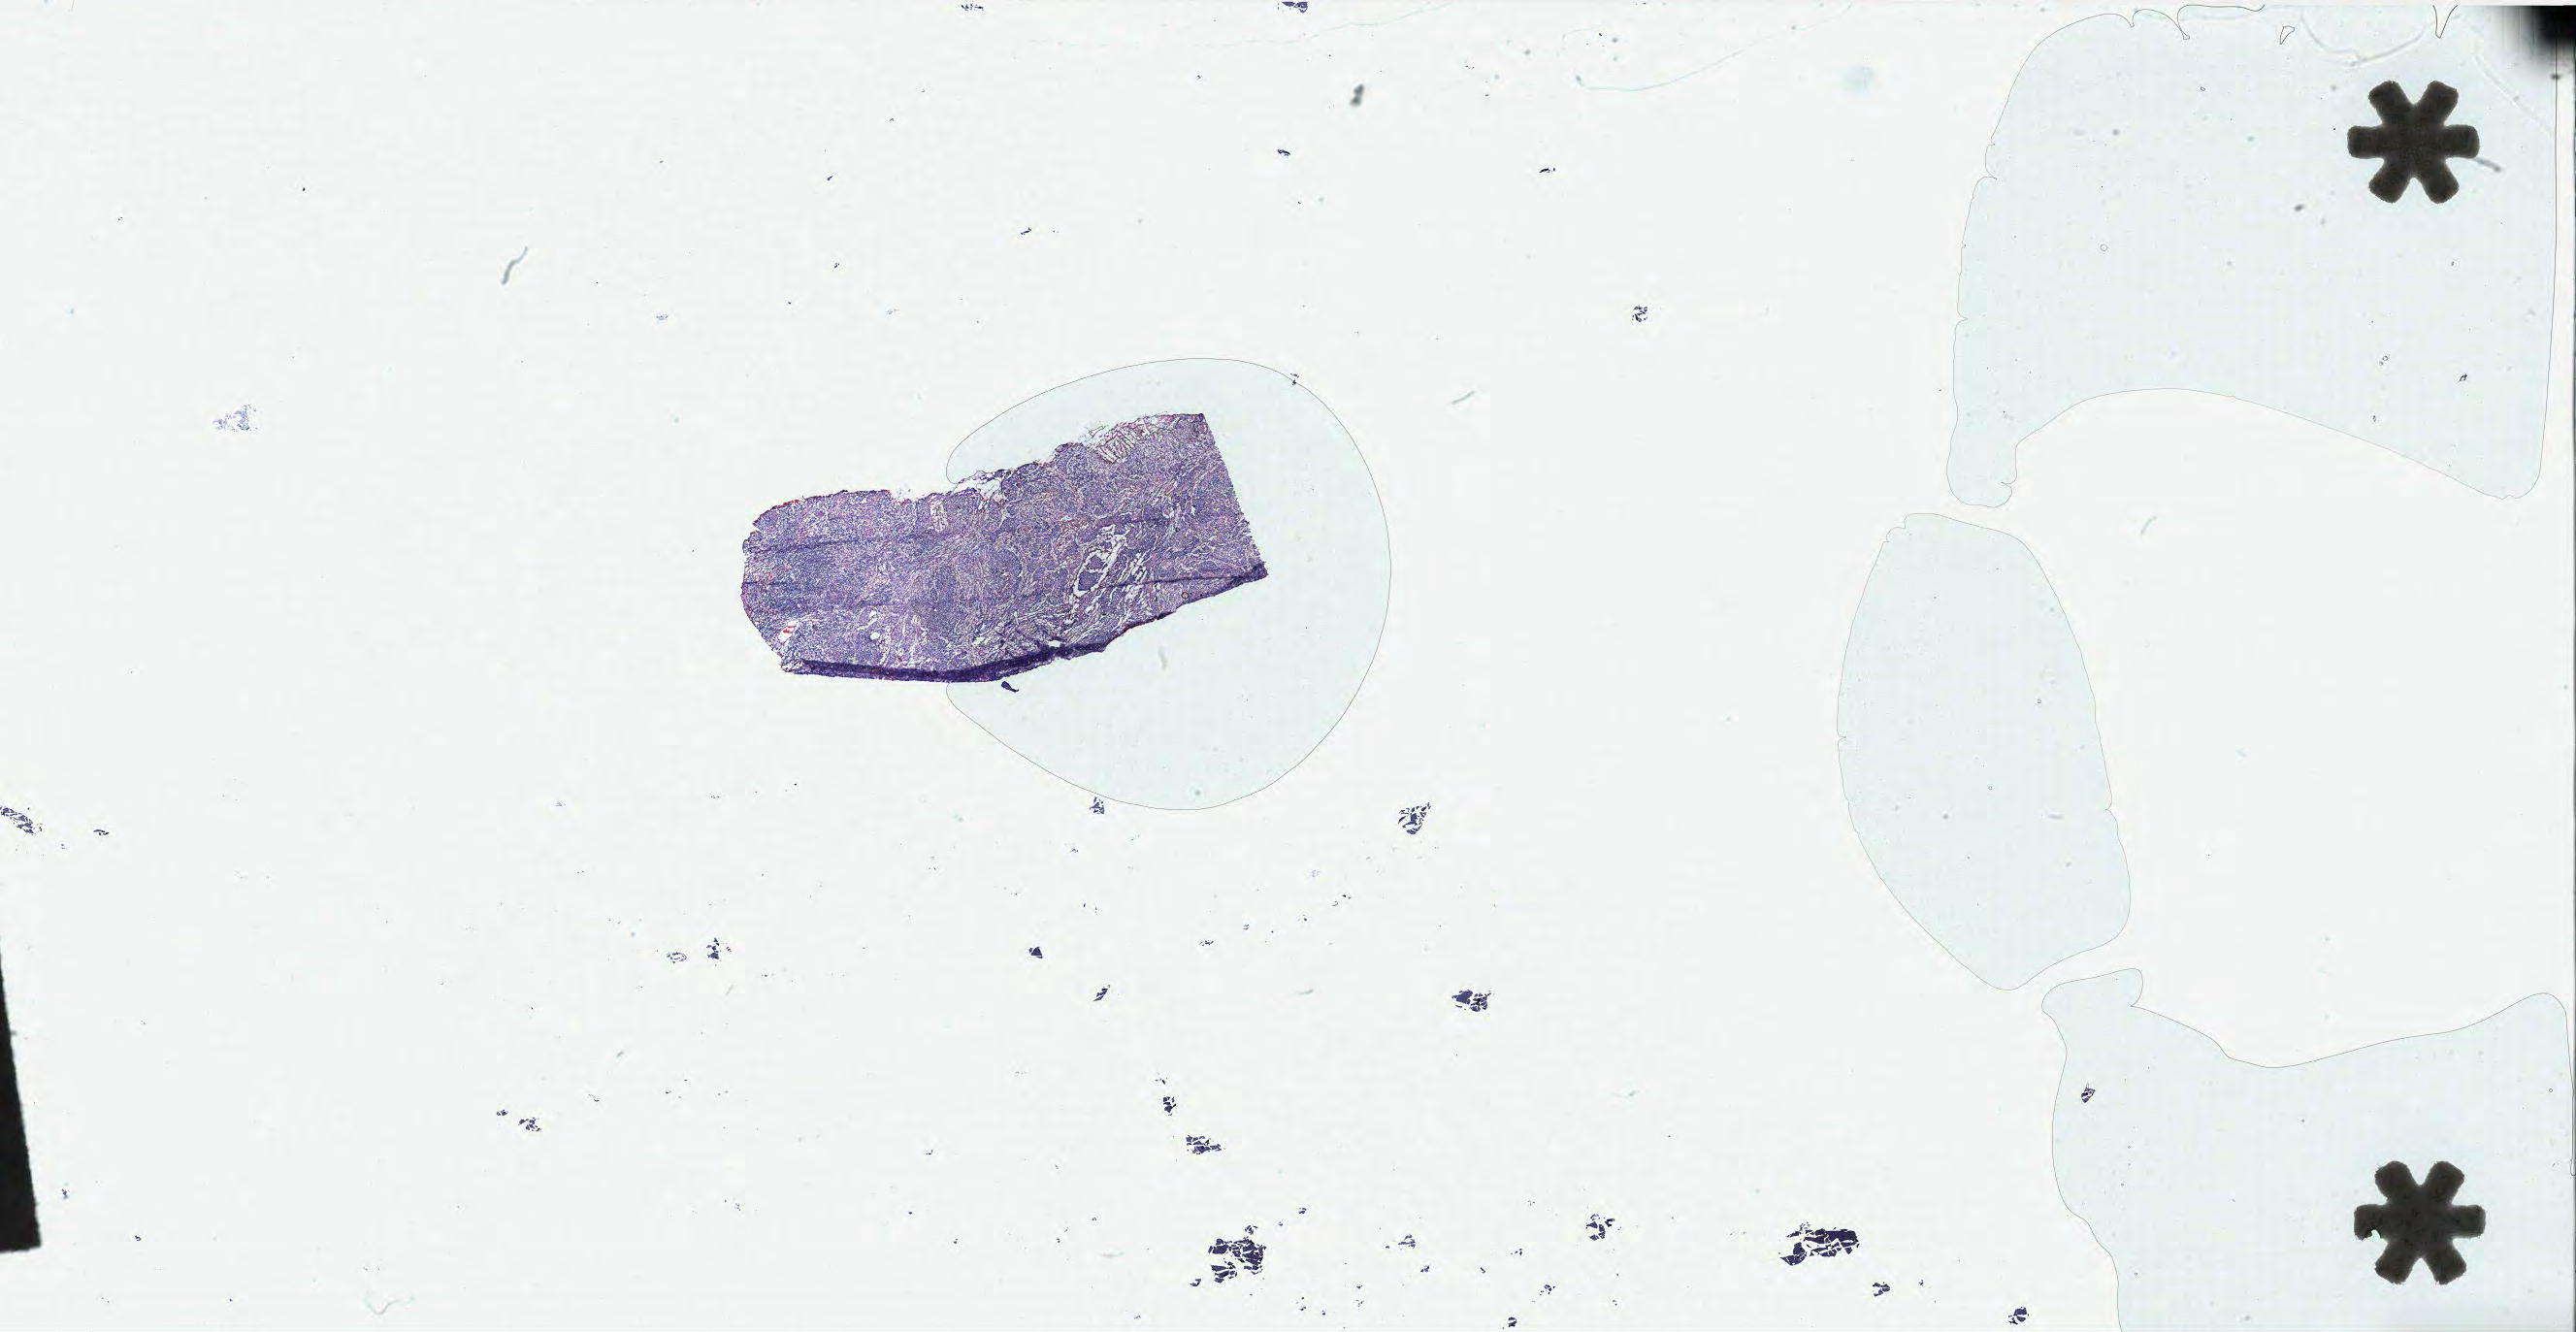
H&E-stained whole-slide image, low-resolution overview of the scanned area, about 42.5 x 22.0 mm (acquisition: 40x scan). FFPE section. Primary tumour sample from the cervix. Female, age 37 years at initial diagnosis. Histologic grade: G3 (poorly differentiated).
Diagnosis: Squamous cell carcinoma, keratinizing, NOS (cervix uteri). FIGO stage: IB1. Lymph nodes positive (case pathology): 0 of 13 examined.